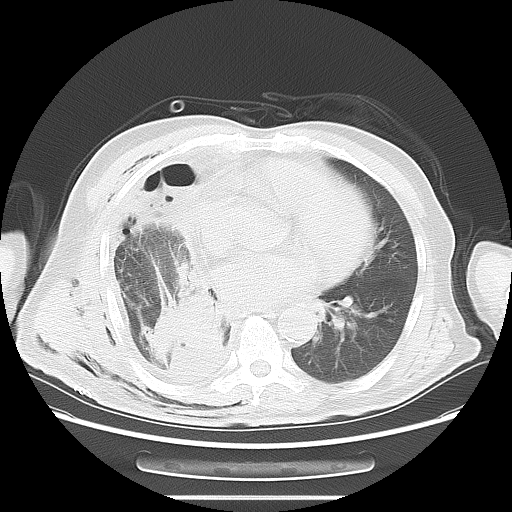
Chest CT, one axial slice; slice 29 of 59 in the series (ordered by position); 120 kVp; lung window (W 1500 / L -600 HU); 5 mm slice thickness; 512 × 512 image matrix, field of view 392 × 392 mm. Patient: male, 69 years. From the clinical record (not read from this slice): clinical TNM (as recorded): T3 N0 M0; histopathological grade: G2-3.
Structures marked on this image (bounding box drawn by a radiologist):
- lung tumour (recorded histology: squamous cell carcinoma): bounding box (x1, y1, x2, y2) in pixels: (137, 286, 243, 398)